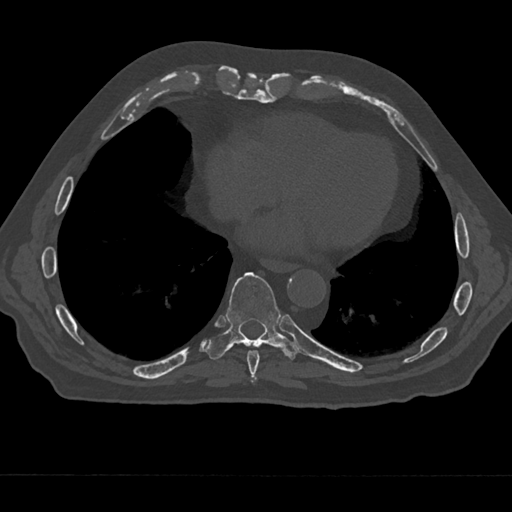
CT including the spine, one axial slice; slice 278 of 797 in the series (ordered by position); bone window (W 1800 / L 400 HU); 0.5 mm slice thickness; 512 × 512 image matrix, field of view 377 × 377 mm. Male patient, age 75 years. Case-level facts recorded for this patient, not image findings: primary cancer: renal.
Annotated regions visible in this slice (semi-automatic segmentation, software-assisted and operator-edited):
- T8 vertebra: bounding box (x1, y1, x2, y2) in pixels: (246, 350, 260, 380)
- T9 vertebra: (206, 272, 297, 359)